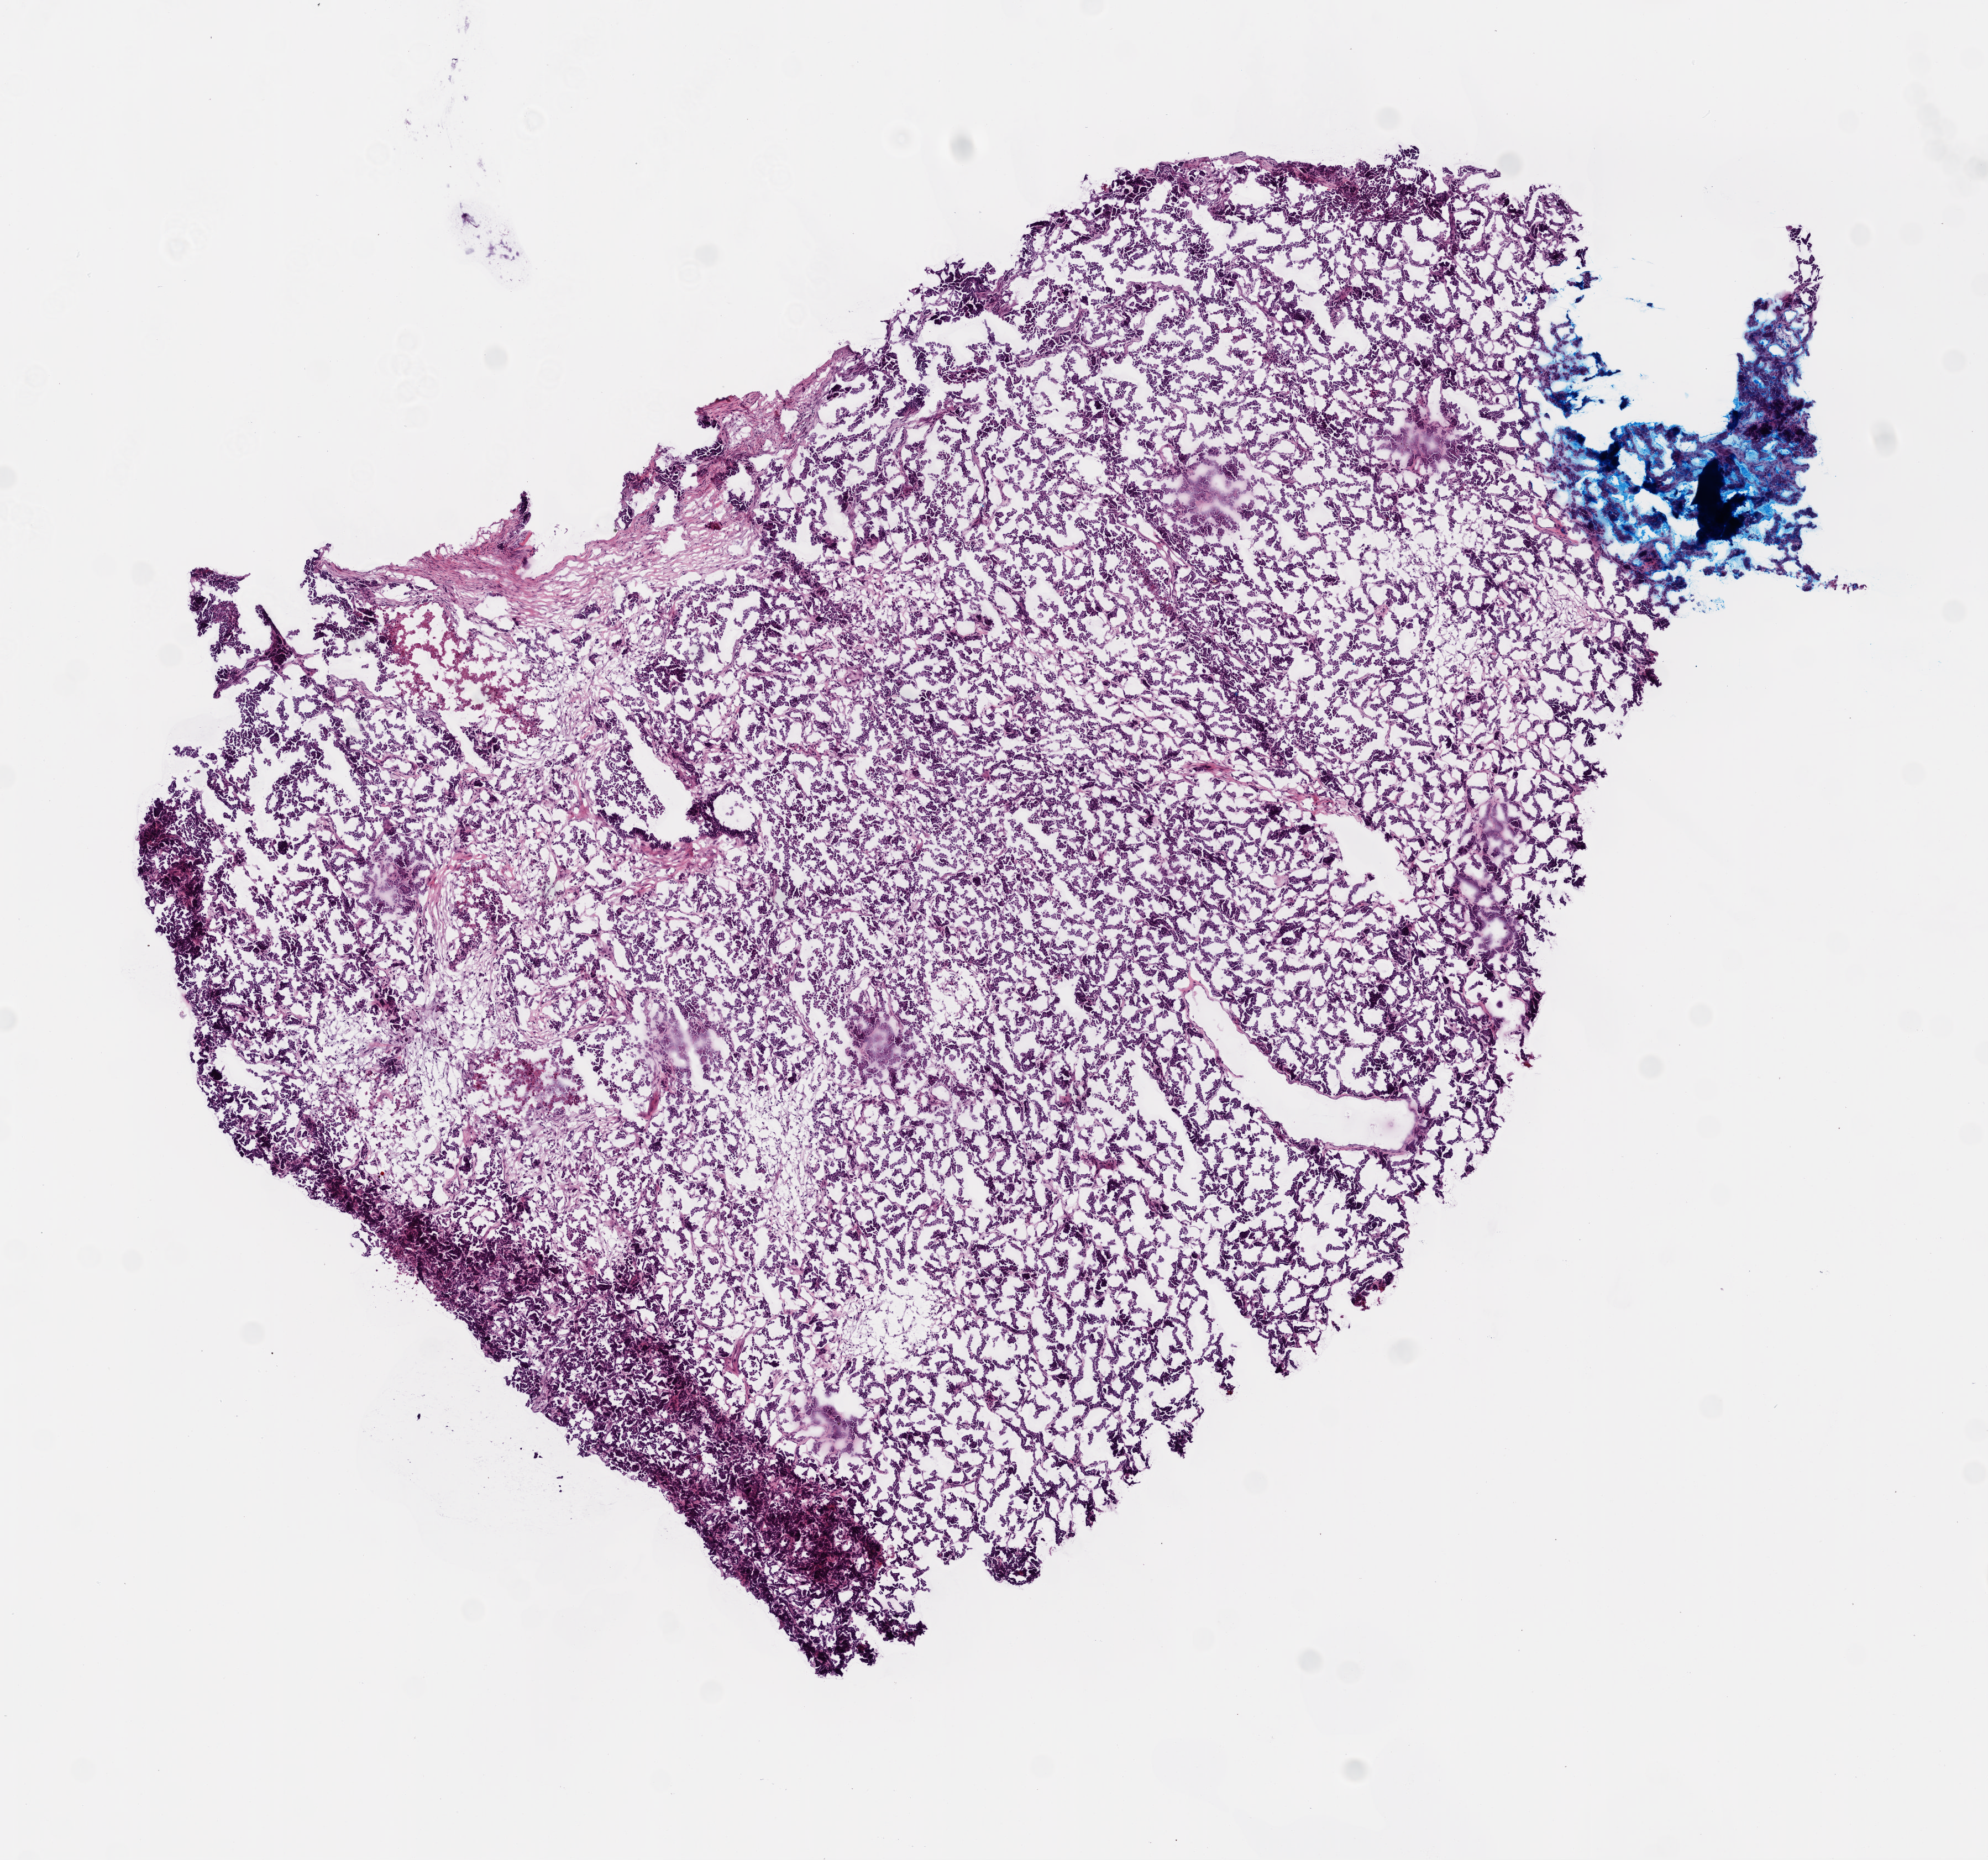
Whole-slide histology image, H&E, shown as a low-resolution overview of the whole scanned area (about 7.3 x 6.8 mm, slide scanned at 20x). Frozen section from the top of the tissue portion. Ovary, primary tumour sample. Female, age 48 years at initial diagnosis. Histologic grade: G3 (poorly differentiated). Slide review estimates, as recorded: tumour nuclei 95%, normal cells 0%, necrosis 5%.
- histologic diagnosis: Serous cystadenocarcinoma, NOS
- FIGO stage: IV